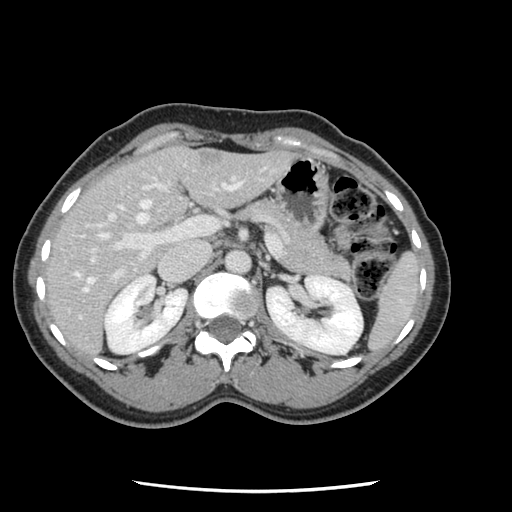
Contrast-enhanced abdominal CT, one axial slice; slice 68 of 134 in the series (ordered by position); 120 kVp; soft-tissue window (W 400 / L 40 HU); 512 × 512 image matrix, field of view 330 × 330 mm. Female patient, age 43 years. Case-level facts recorded for this patient, not image findings: diagnosis: colorectal cancer liver metastases, imaged before liver resection; multiple liver metastases: yes; largest metastasis: 3.4 cm; disease in both lobes: yes.
Structures marked on this image (outlined manually by an expert reader):
- hepatic veins: bounding box [x1, y1, x2, y2] px = [75, 182, 238, 292]
- liver: [47, 147, 293, 355]
- planned liver remnant (the part of the liver to remain after resection): [46, 150, 186, 304]
- portal vein (with intrahepatic branches): [69, 177, 235, 311]
- liver metastasis: [199, 155, 222, 165]